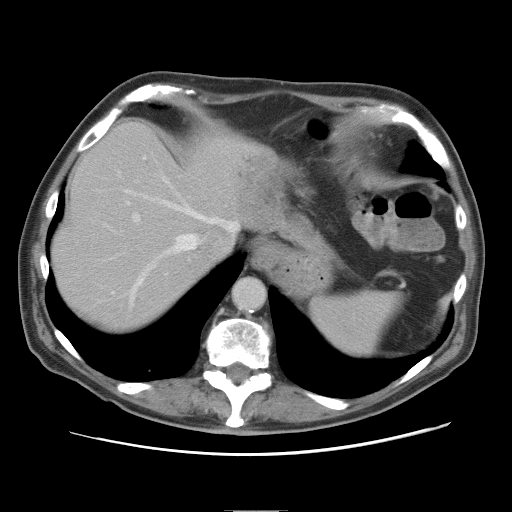
Contrast-enhanced abdominal CT, one axial slice. Position 65 of 89 along the scan axis. 120 kVp. Intravenous contrast given. Soft-tissue window (W 400 / L 40 HU). 5 mm slice thickness. 512 × 512 image matrix, field of view 375 × 375 mm. Male patient, age 69 years. Case-level facts recorded for this patient, not image findings: diagnosis: colorectal cancer liver metastases, imaged before liver resection; multiple liver metastases: no; largest metastasis: 8.5 cm; disease in both lobes: no.
Outlined on this slice (expert manual segmentation):
- hepatic veins: bounding box <123,175,239,302> (left, top, right, bottom; pixels)
- liver: <54,124,282,328>
- planned liver remnant (the part of the liver to remain after resection): <54,125,241,329>
- portal vein (with intrahepatic branches): <133,157,146,223>
- liver metastasis: <247,160,292,215>